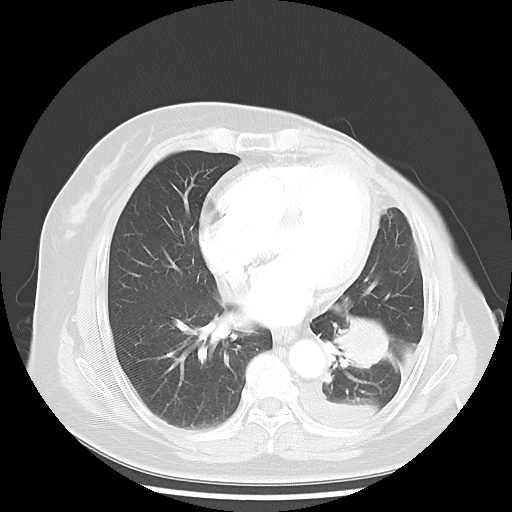
Chest CT, one axial slice; slice 18 of 48 in the series (ordered by position); reconstruction kernel LUNG; 120 kVp; lung window (W 1500 / L -600 HU); 512 × 512 image matrix, field of view 360 × 360 mm. Female patient, age 63 years. From the clinical record (not read from this slice): clinical TNM (as recorded): T2 N0 M1.
Outlined on this slice (bounding box drawn by a radiologist):
- lung tumour (recorded histology: adenocarcinoma): box from (x=333, y=306) to (x=390, y=376) px